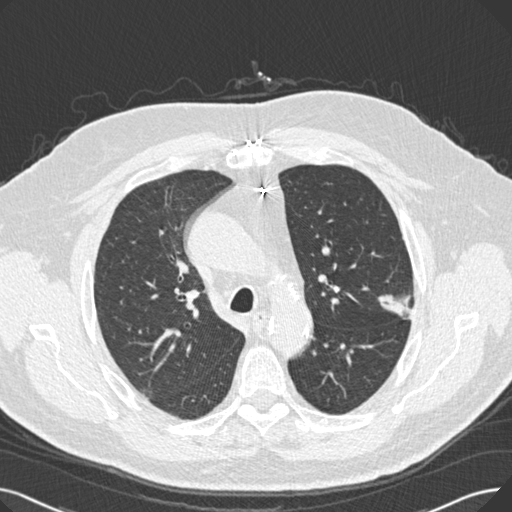
Low-dose screening chest CT, one axial slice. Reconstruction kernel B30f. Lung window (W 1500 / L -600 HU). 1 mm slice thickness. 512 × 512 image matrix, field of view 370 × 370 mm.
Structures marked on this image (manually delineated by an expert):
- lesion 1 (tumor, upper lobe of left lung): box from (x=378, y=295) to (x=411, y=319) px